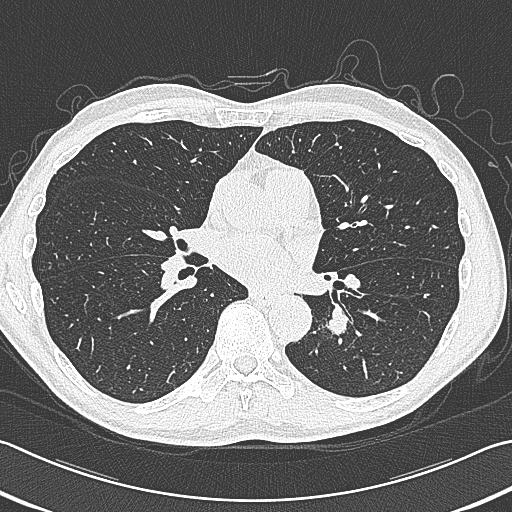
Chest CT (low-dose screening protocol), one axial image, first (baseline) screen, lung window (W 1500 / L -600 HU), lung (sharp) reconstruction kernel (B80f), 120 kVp, slice 182 of 354 in the series, 512 × 512 image matrix, field of view 346 × 346 mm. Male, age 59 years at enrolment. Former smoker at enrolment.
- Lesion marked by an expert reader, bounding box [x1, y1, x2, y2] px = [312, 296, 376, 353].
- The exam's reader record, not a measurement of the box and not confirmed to be the same lesion: non-calcified nodule or mass ≥4 mm, left lower lobe, 15 × 15 mm, smooth margins, soft tissue attenuation.
- Official screen result: positive, change unspecified: nodule(s) >= 4 mm or enlarging nodule(s), mass(es), or other non-specific abnormalities suspicious for lung cancer.
- Participant outcome: lung cancer diagnosed 17 days after this screen — squamous cell carcinoma, large cell, nonkeratinizing, NOS, left lower lobe, poorly differentiated (G3), stage IB (AJCC 6th edition), 31 mm at pathology.